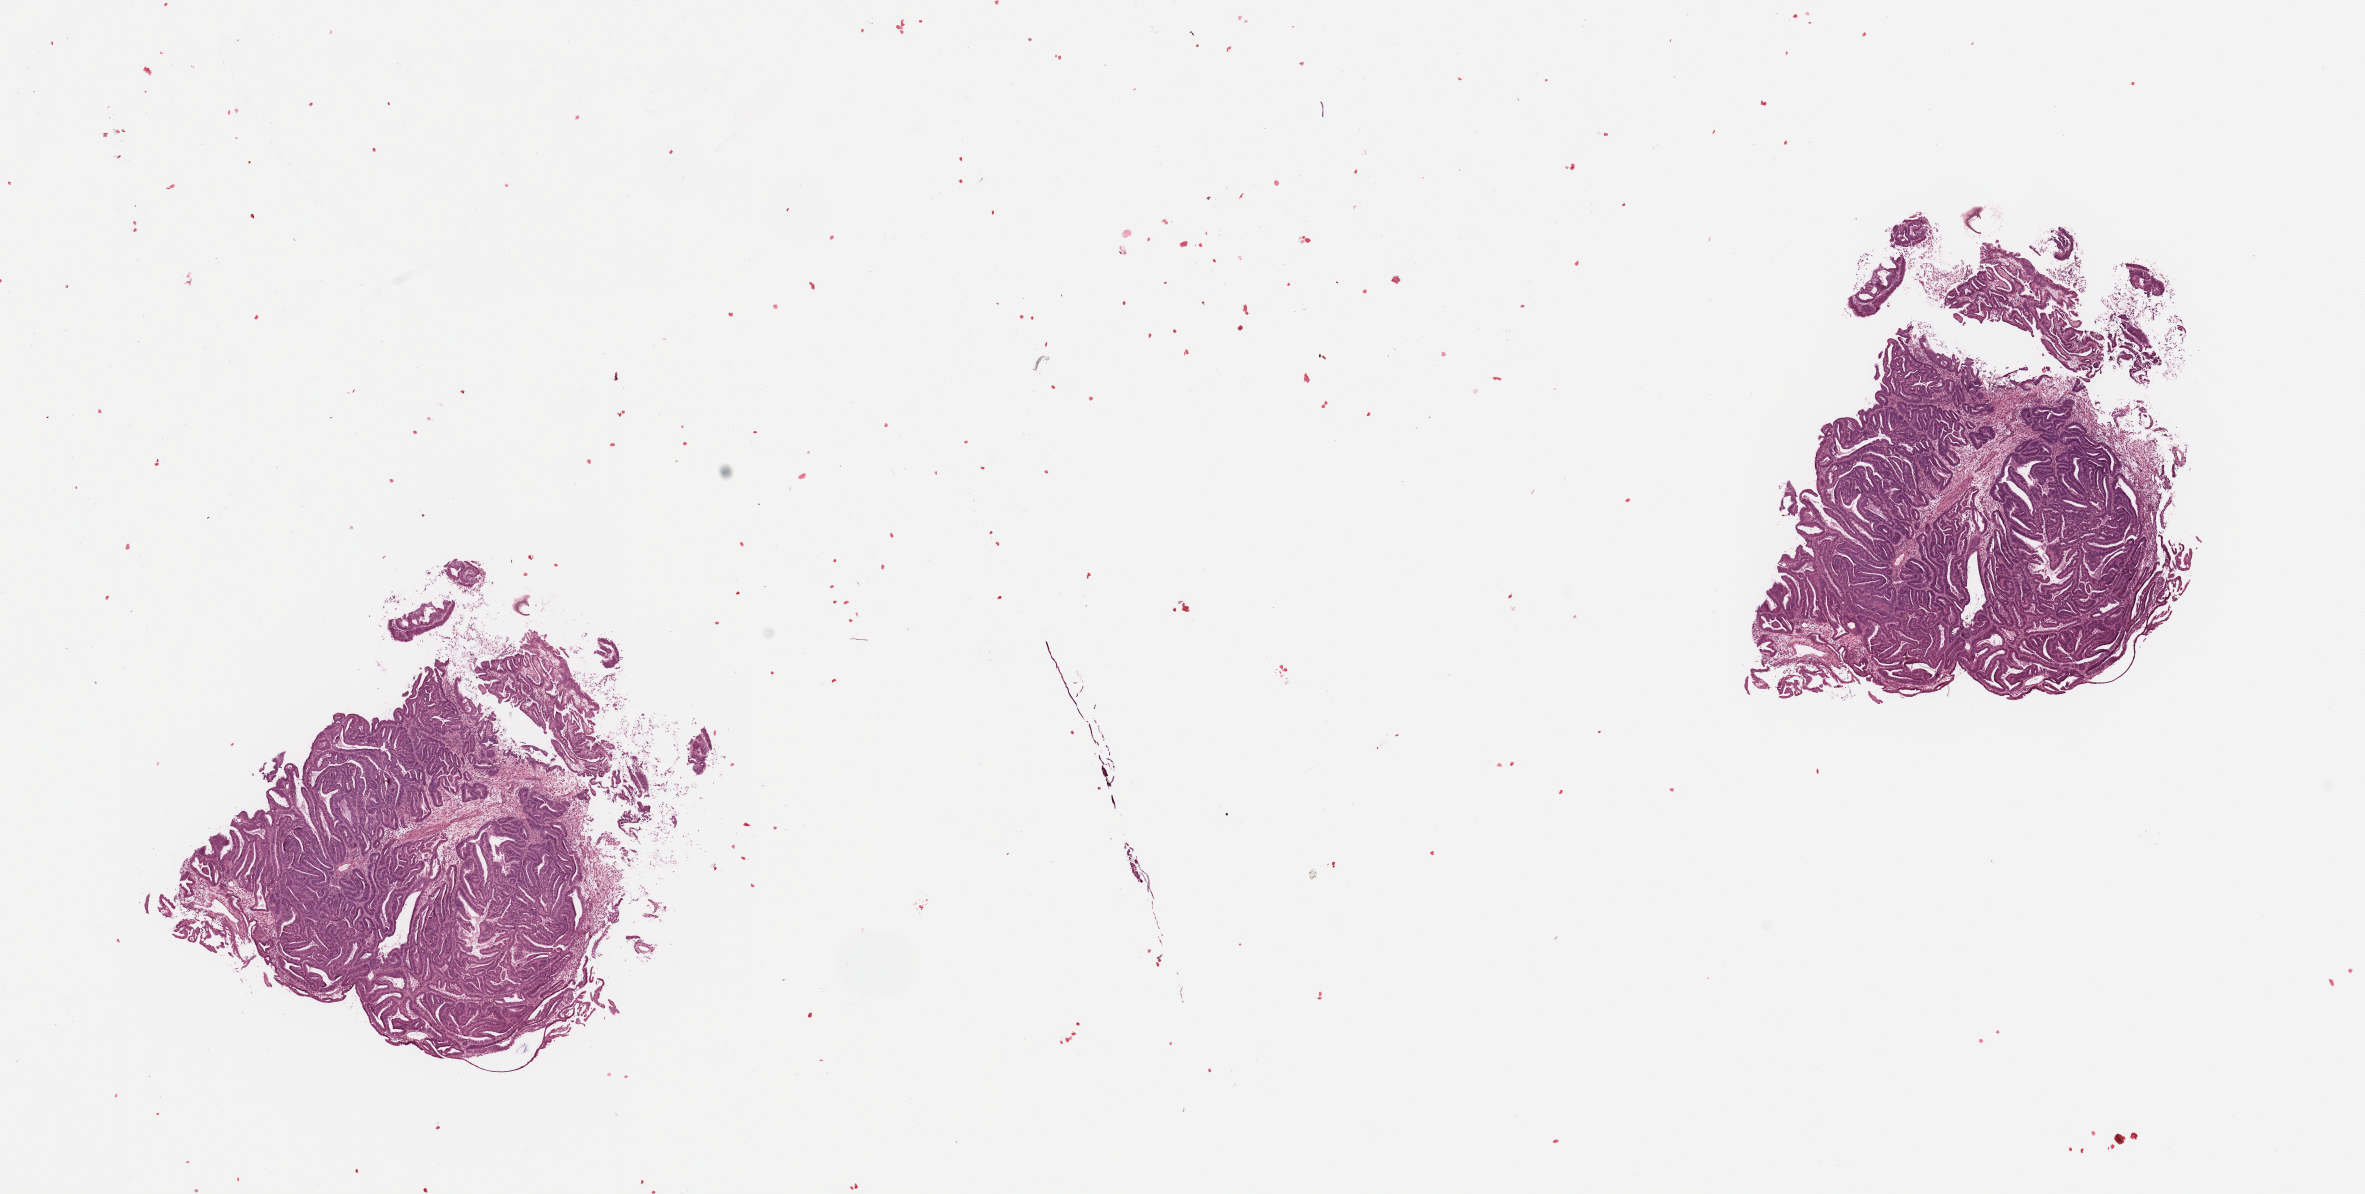
H&E whole-slide image, low-resolution overview of the scanned area, about 18.7 x 9.4 mm, tumour tissue sample, uterus. 68-year-old female patient. Histologic grade: G2 (moderately differentiated).
AJCC pathologic stage: I. Histologic diagnosis: Endometrioid adenocarcinoma, NOS. Primary tumour site (as recorded): anterior endometrium.